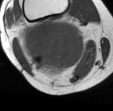
MRI of an extremity soft-tissue mass, one axial slice; position 31 of 45 along the scan axis; MR volume resampled by the dataset authors to the PET/CT grid (not the native acquisition matrix); 3.27 mm slice thickness; 113 × 111 image matrix. Female patient. From the clinical record (not read from this slice): histological type: liposarcoma; site of the primary tumour: right thigh.
Annotated regions visible in this slice (expert contour drawn on MRI and transferred to this co-registered scan by the dataset authors):
- gross tumour volume (mass): box from (x=17, y=19) to (x=88, y=79) px